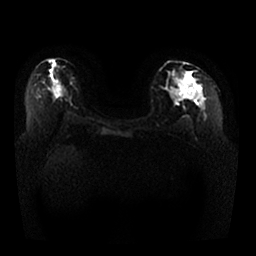
Breast MRI, one axial slice. Position 15 of 25 along the scan axis. Diffusion-weighted series; image 2 of 4 stored at this slice position (different b-values; order by instance number). 1.5 T. 4 mm slice thickness. 256 × 256 image matrix, field of view 350 × 350 mm. Female patient.
Annotated regions visible in this slice (outlined manually by an expert reader):
- tumour on diffusion-weighted imaging: box from (x=176, y=84) to (x=195, y=99) px